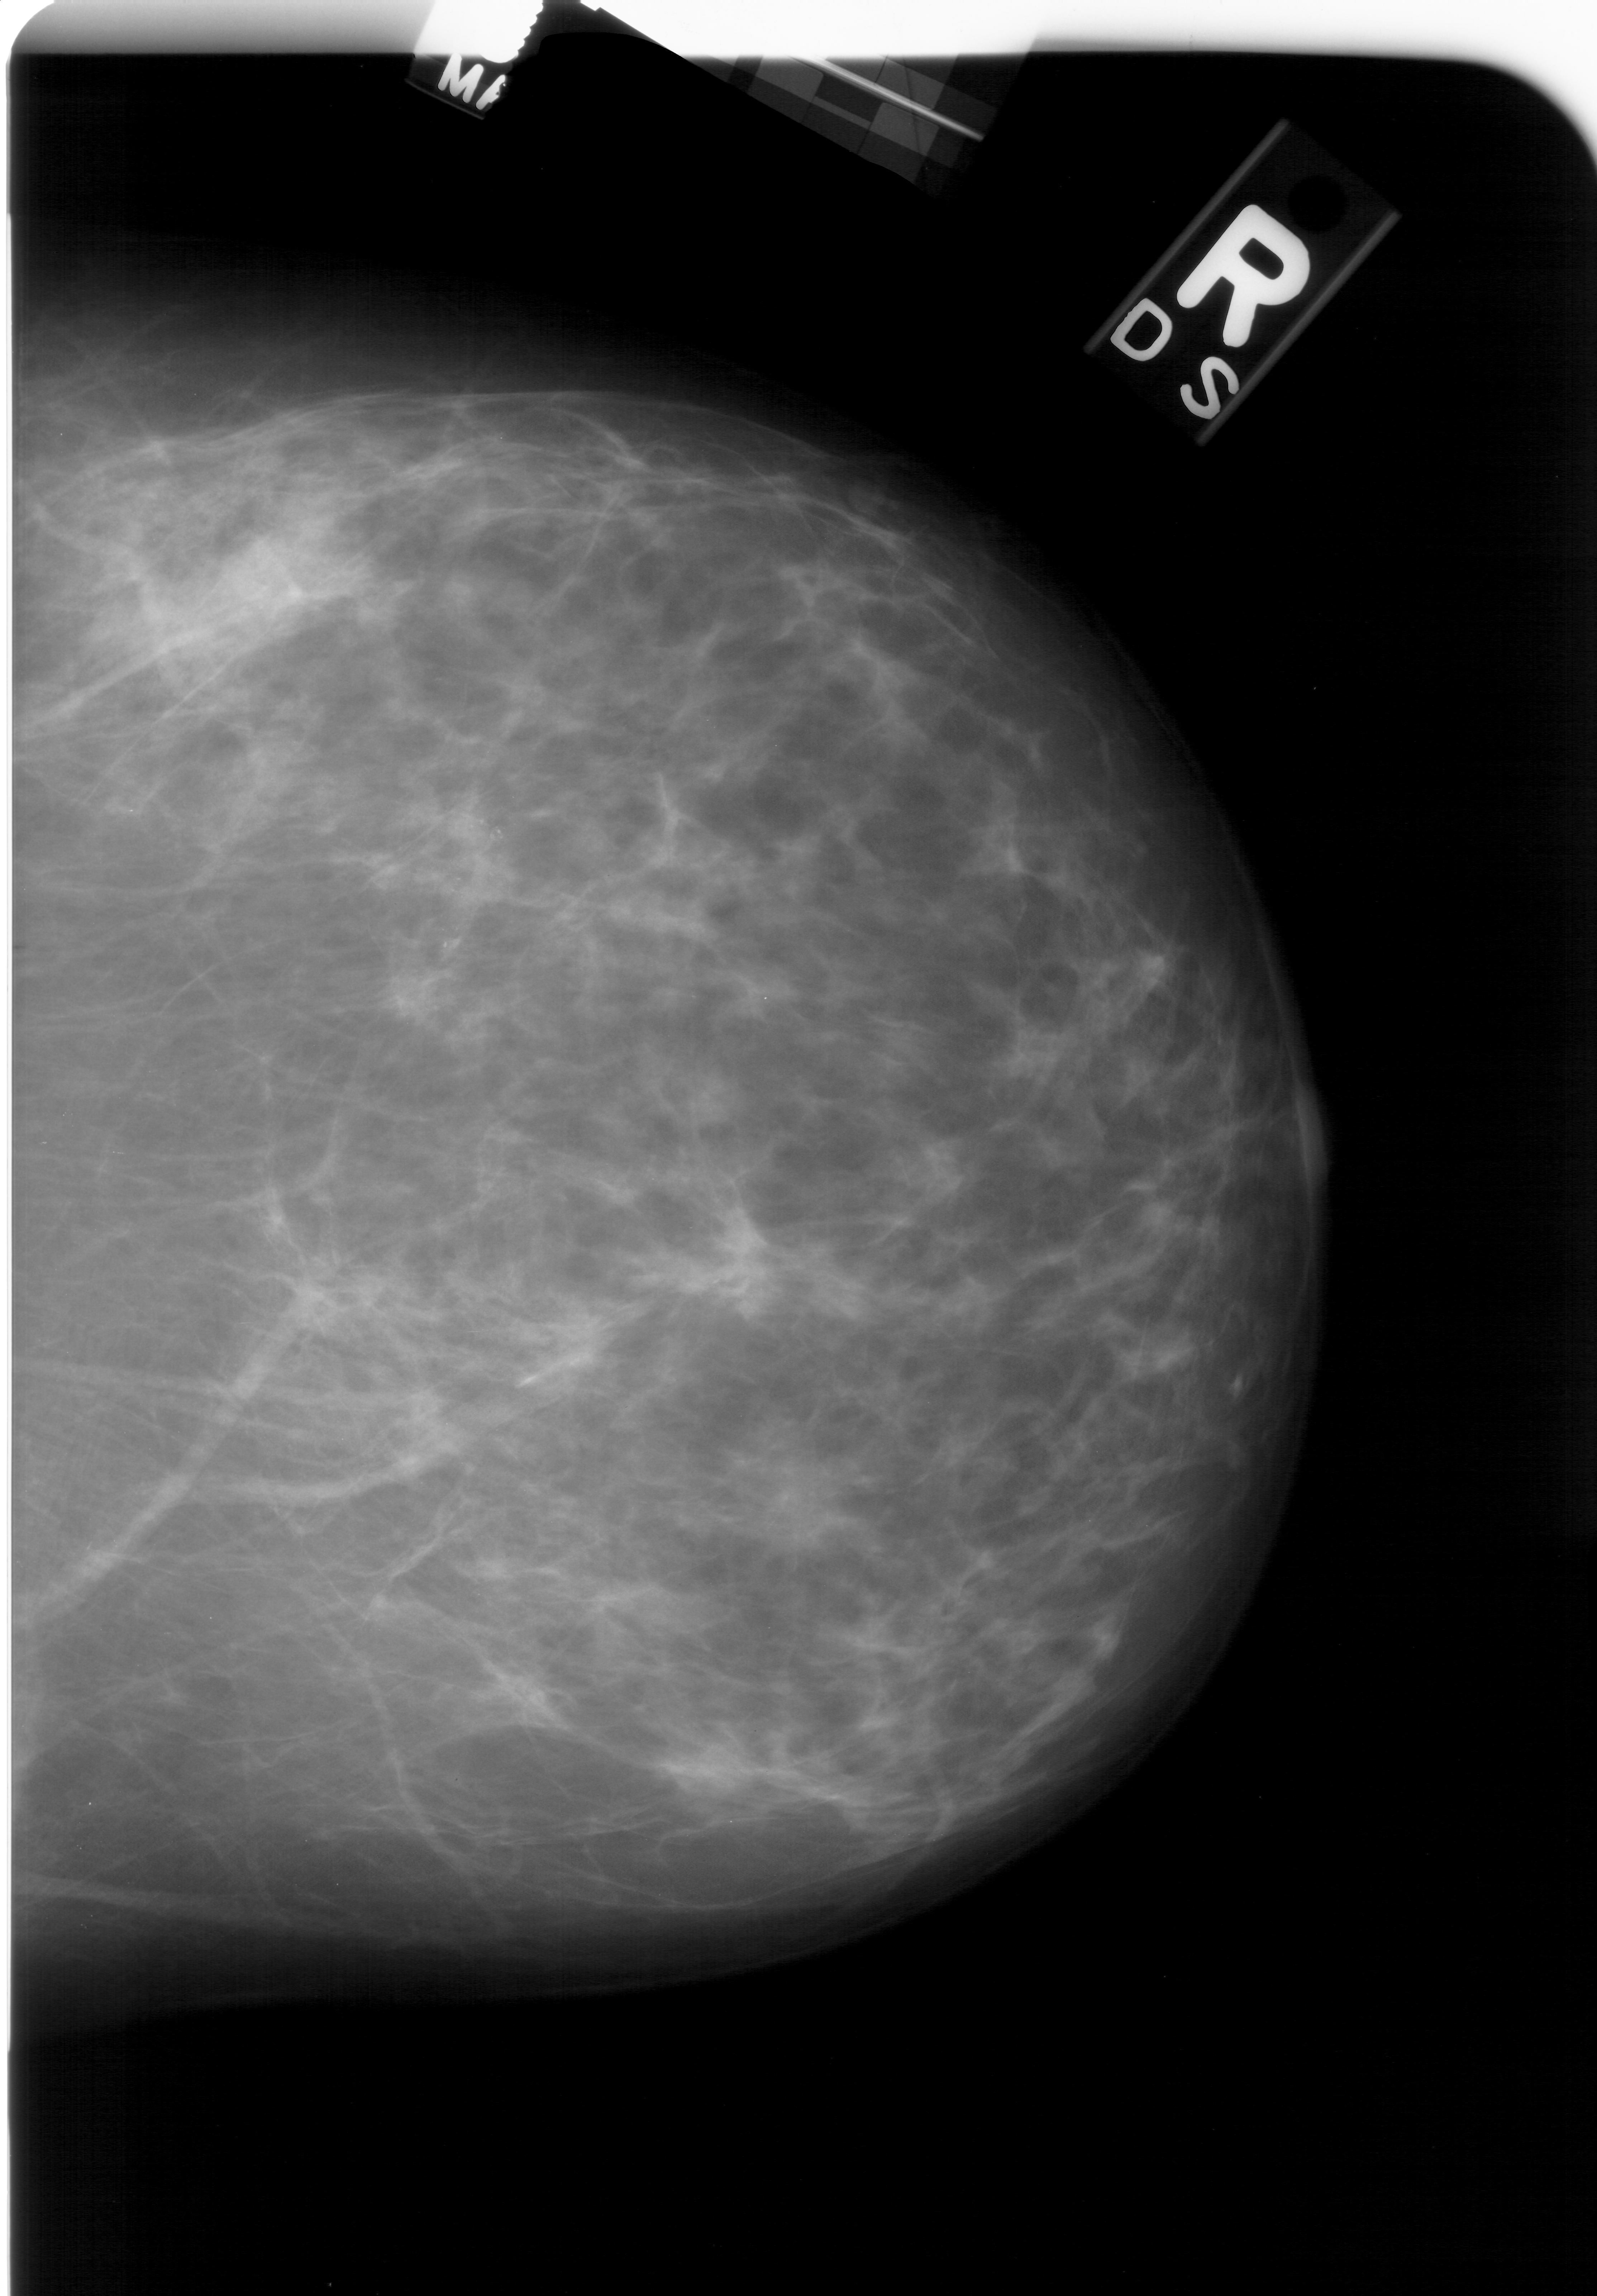
Mammogram (digitized film), right breast, craniocaudal (CC) view.
- Marked abnormality: calcifications, morphology pleomorphic, distribution linear; BI-RADS assessment category 4; pathology result (as recorded, not read from the image): malignant.